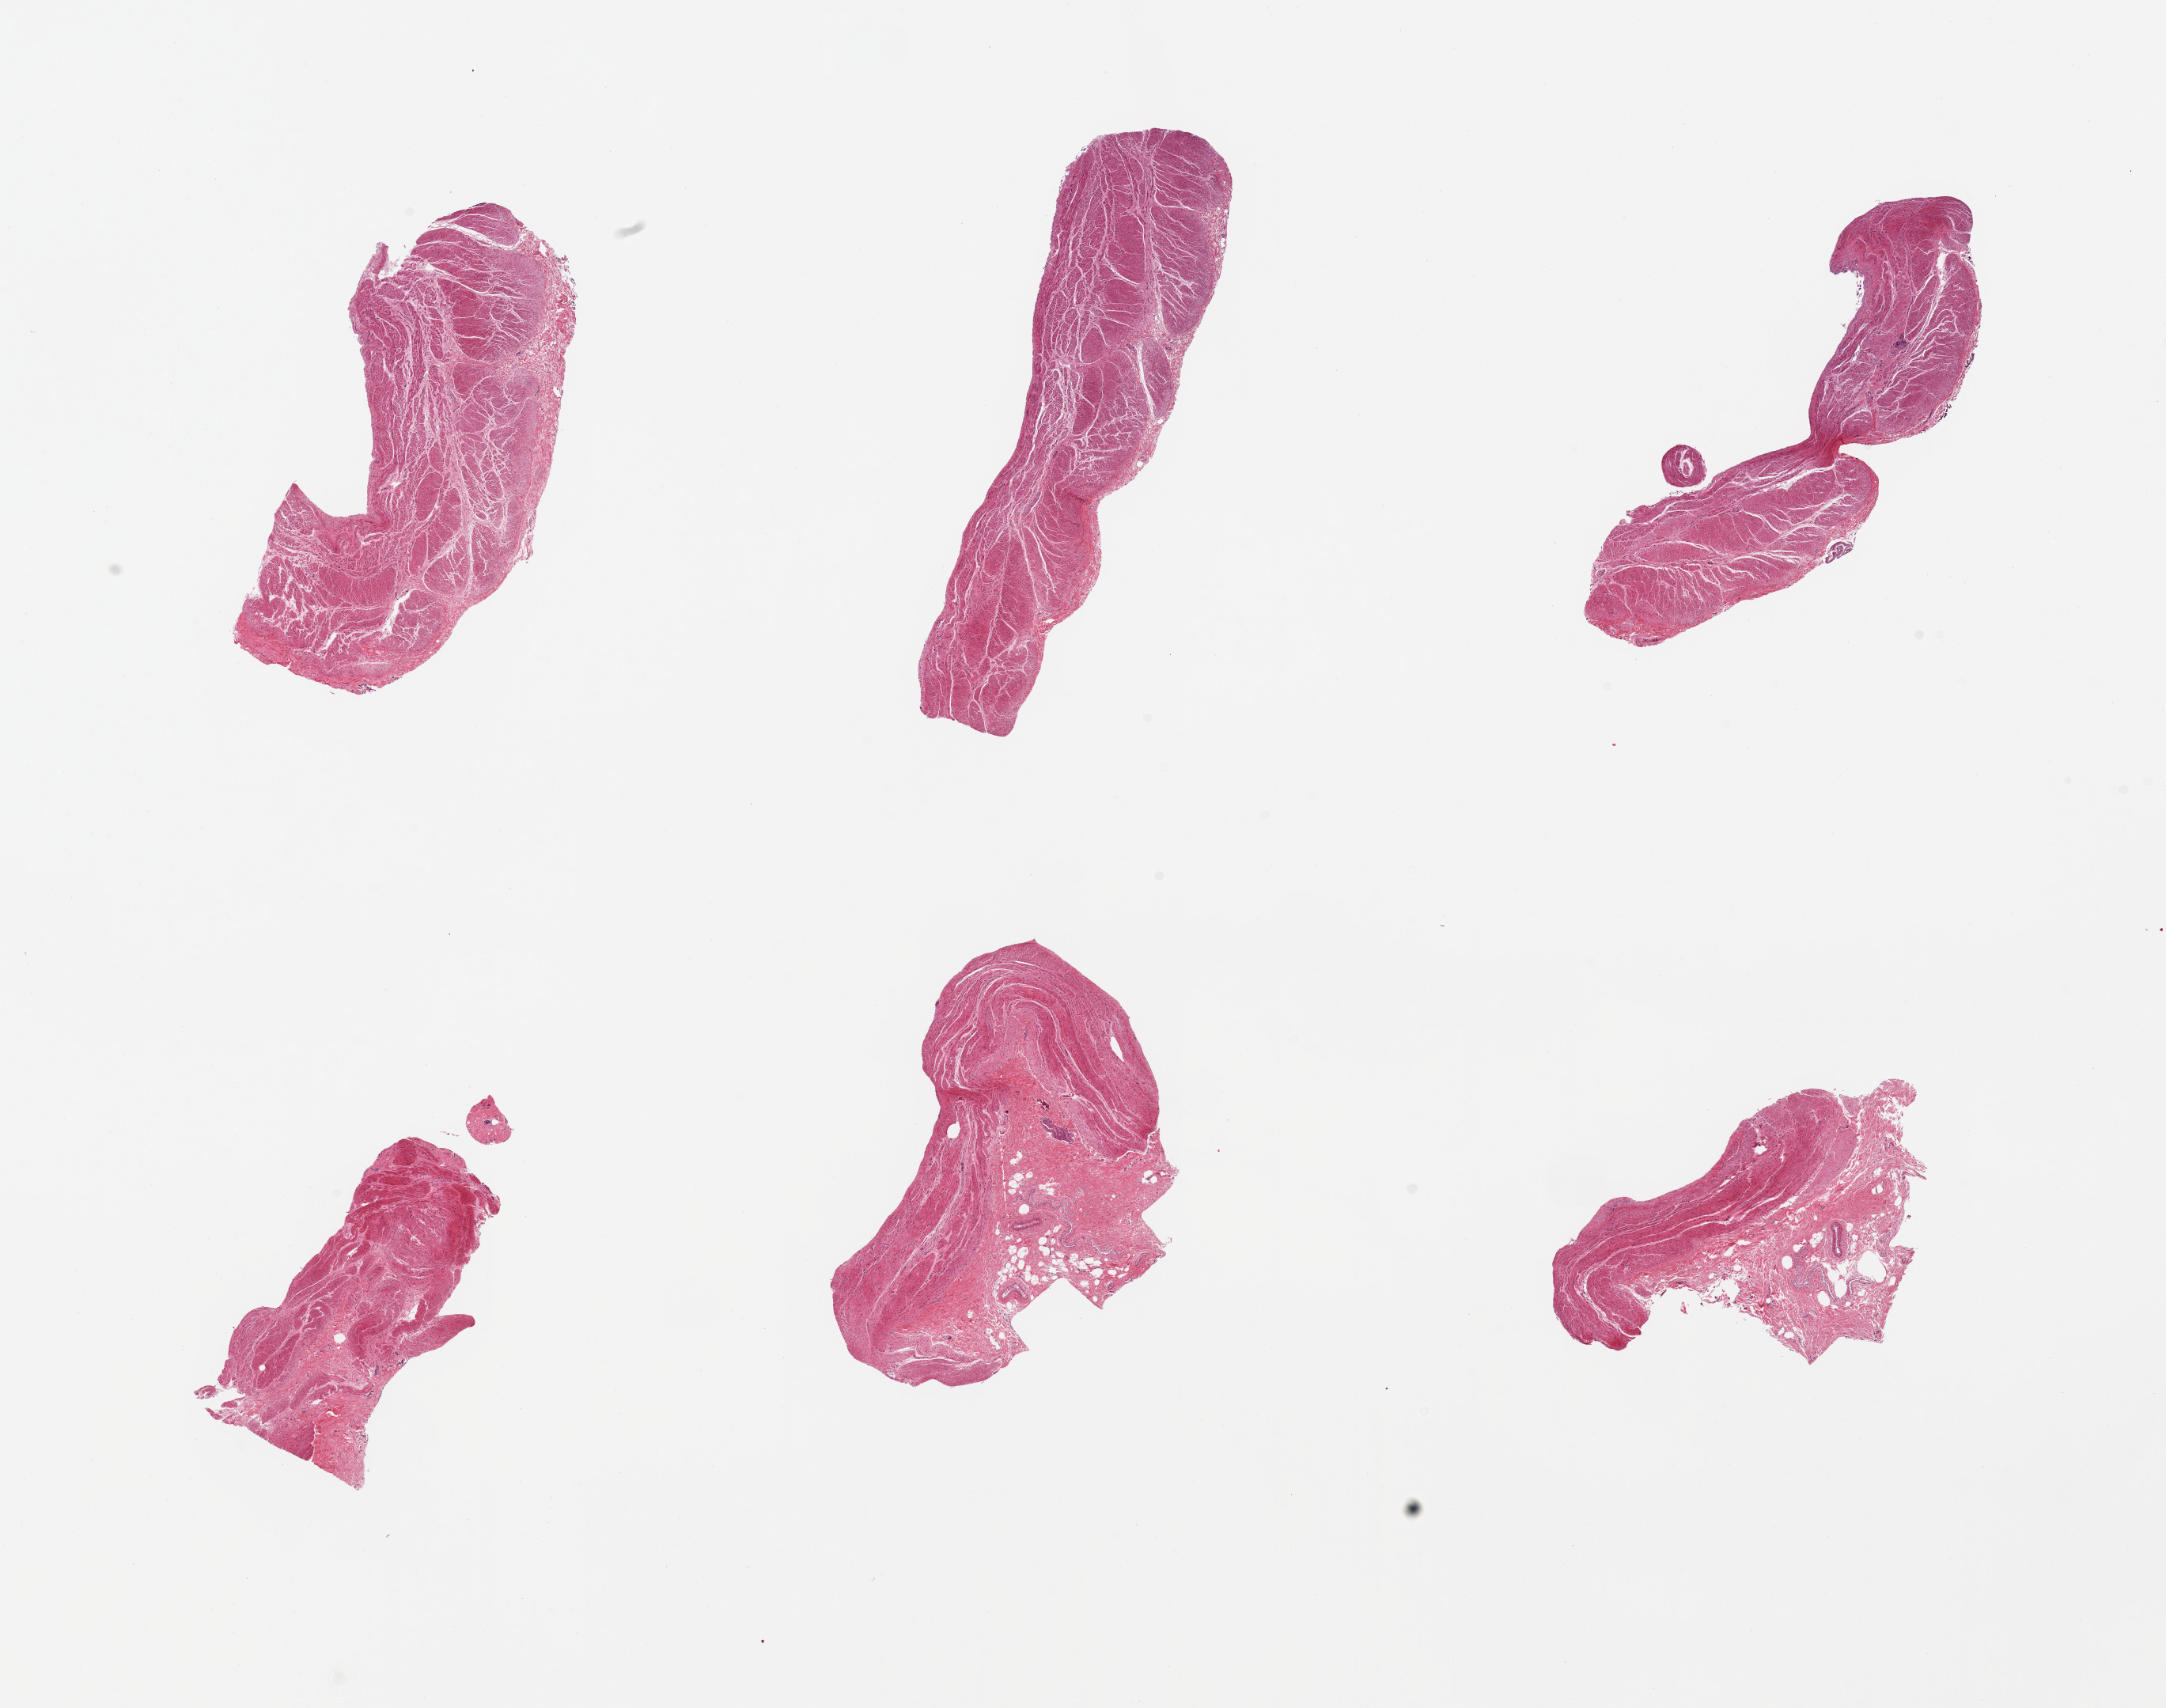
Digitized haematoxylin and eosin-stained section, low-resolution overview of the scanned area, about 21.7 x 17.1 mm, PAXgene-fixed, paraffin-embedded tissue, target tissue: stomach, donor tissue sample. Donor sex: male.
* review note (as recorded): 6 pieces; only muscle no mucosa; 2 pieces have up to 50% submucosal stroma